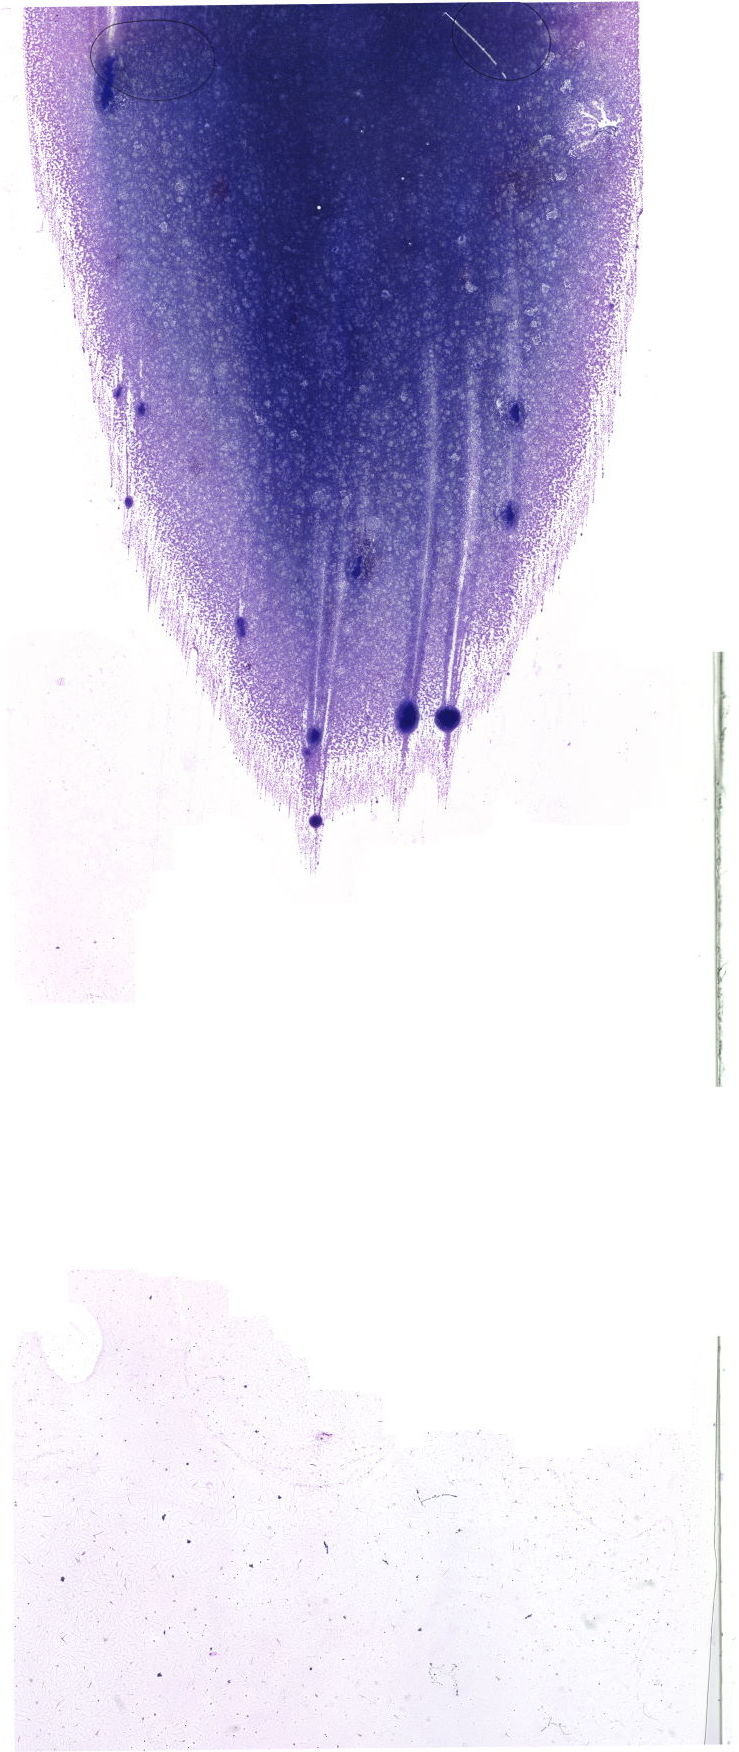
Whole-slide image of a May-Grünwald-Giemsa (MGG)-stained bone marrow aspirate smear — low-resolution overview of the scanned area, about 20.9 x 49.7 mm. Patient sex: male.
• diagnosis: Chronic Phase Chronic Myeloid Leukemia, BCR-ABL1 Positive